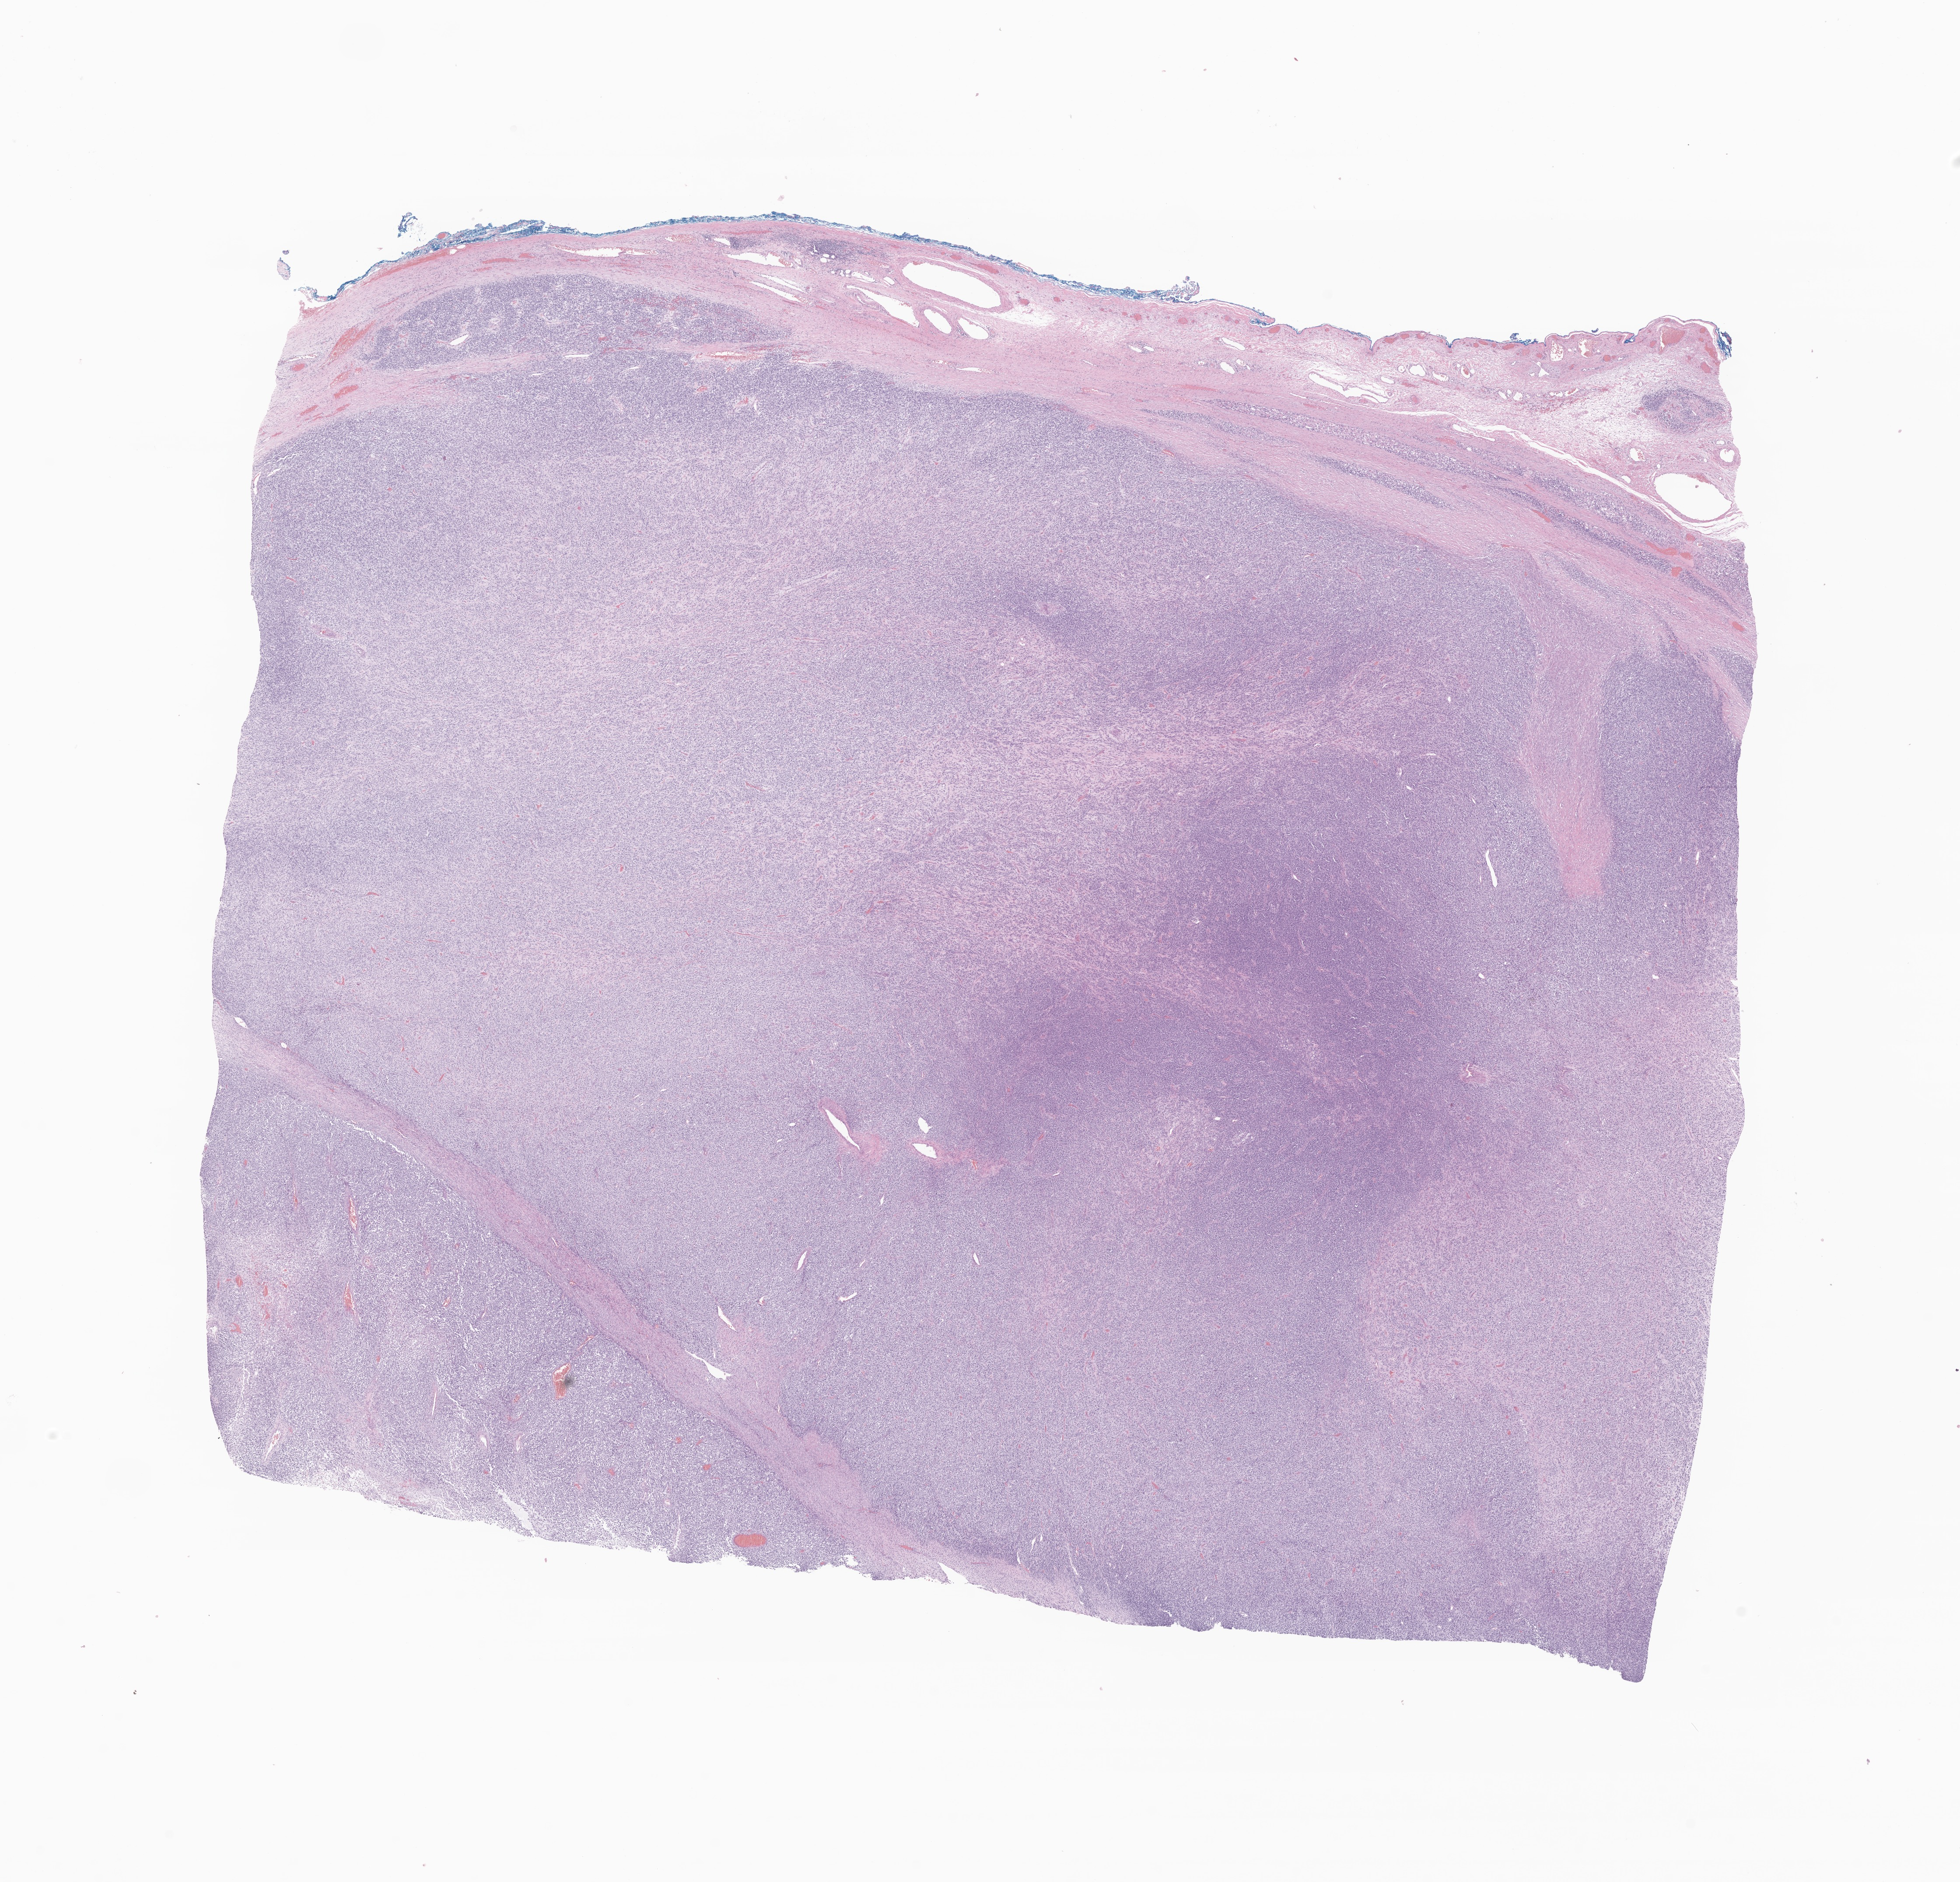
Whole-slide image, H&E stain of tumor tissue from the soft tissue, shown as a low-resolution overview of the whole scanned area (about 18.9 x 18.1 mm). Formalin-fixed, paraffin-embedded (FFPE) tissue. Patient male; age 242 months (20 years 2 months).
• diagnosis (ICD-O-3 morphology term): Embryonal rhabdomyosarcoma, NOS